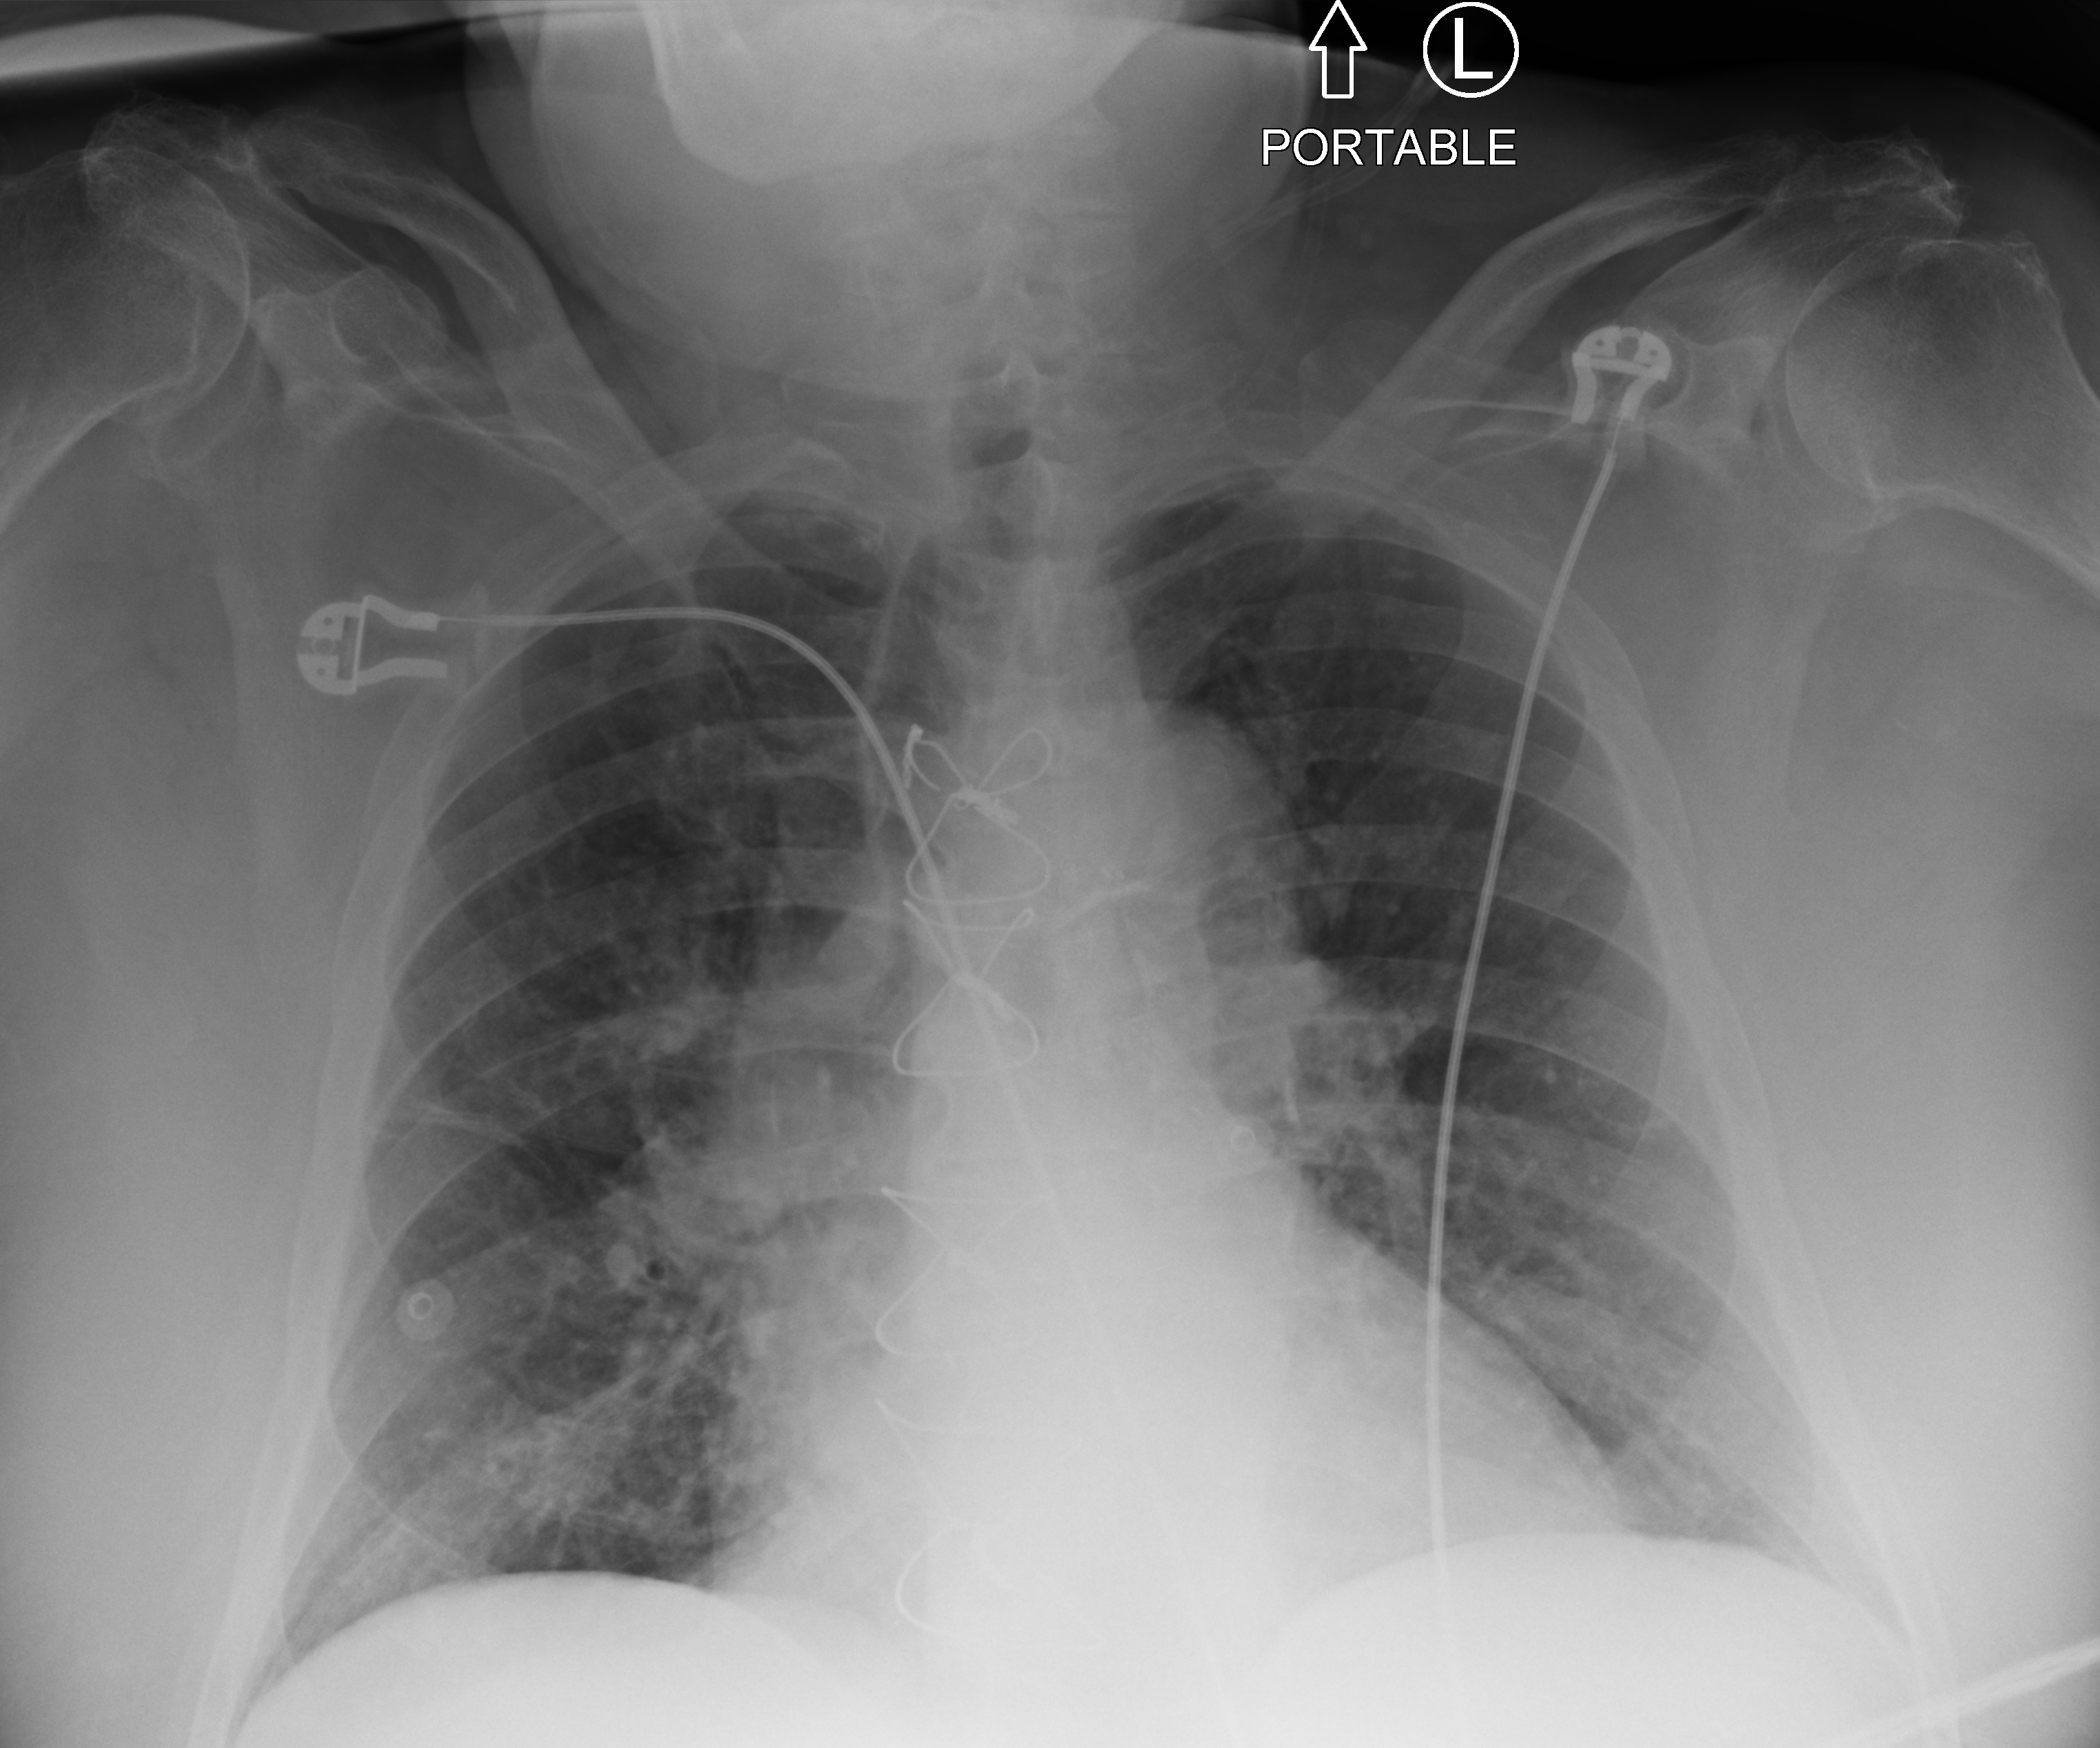
Portable chest radiograph, anteroposterior (AP) projection. Patient hospitalised with COVID-19; male, aged 75–90 years.
Admission-level facts for this patient (not findings on this image; timing relative to this image not recorded):
- diabetes (admission record): yes
- admitted to intensive care during this hospital stay: no